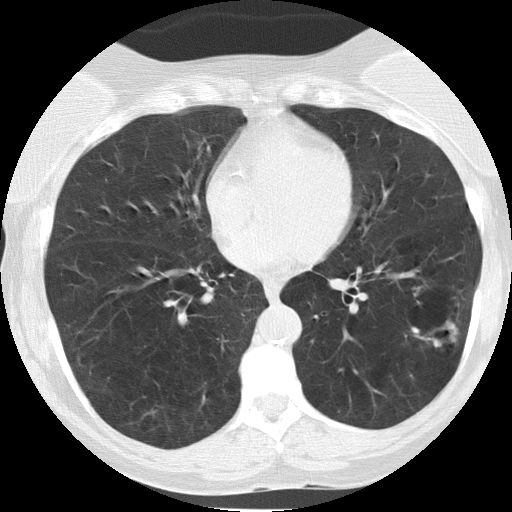
Low-dose screening chest CT, one axial slice. Slice 66 of 149 in the series (ordered by position). Lung window (W 1500 / L -600 HU). 2 mm slice thickness. 512 × 512 image matrix, field of view 290 × 290 mm.
Annotated regions visible in this slice (expert manual segmentation):
- lesion 1 (tumor, lower lobe of left lung): box from (x=412, y=321) to (x=458, y=347) px